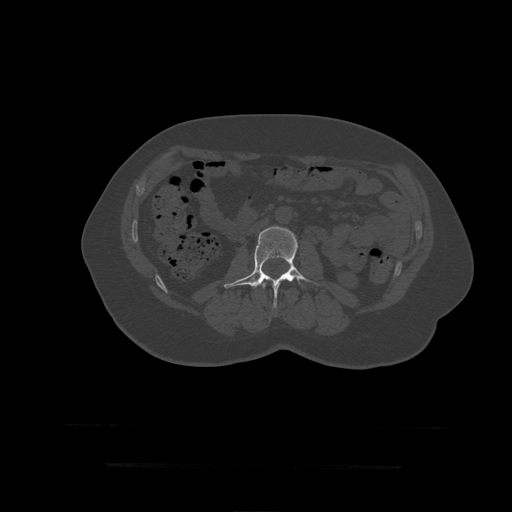
CT including the spine, one axial slice; position 126 of 399 along the scan axis; reconstruction kernel STANDARD; 120 kVp; bone window (W 1800 / L 400 HU); 1.25 mm slice thickness; 512 × 512 image matrix, field of view 450 × 450 mm. Patient age 41 years. Case-level facts recorded for this patient, not image findings: primary cancer: breast.
Outlined on this slice (semi-automatically segmented with operator editing):
- L2 vertebra: box from (x=262, y=282) to (x=267, y=289) px
- L3 vertebra: (x=224, y=227)–(x=320, y=308)